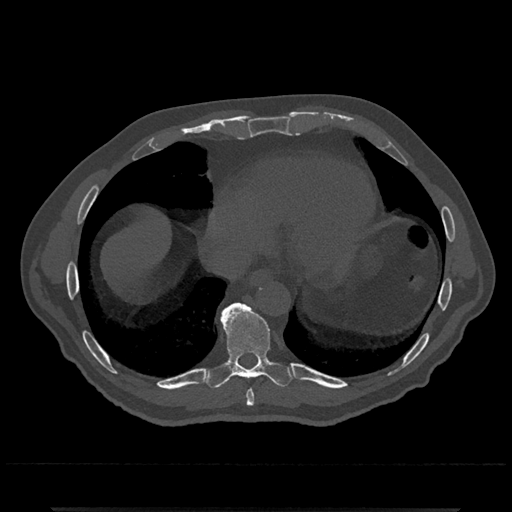
CT including the spine, one axial slice. Position 621 of 797 along the scan axis. Reconstruction kernel Br40s/3. 120 kVp. Bone window (W 1800 / L 400 HU). 0.5 mm slice thickness. 512 × 512 image matrix. Male patient, age 67 years. Case-level facts recorded for this patient, not image findings: primary cancer: prostate.
Annotated regions visible in this slice (semi-automatically segmented with operator editing):
- T8 vertebra: bounding box <246,390,255,407> (left, top, right, bottom; pixels)
- T9 vertebra: <204,303,295,389>